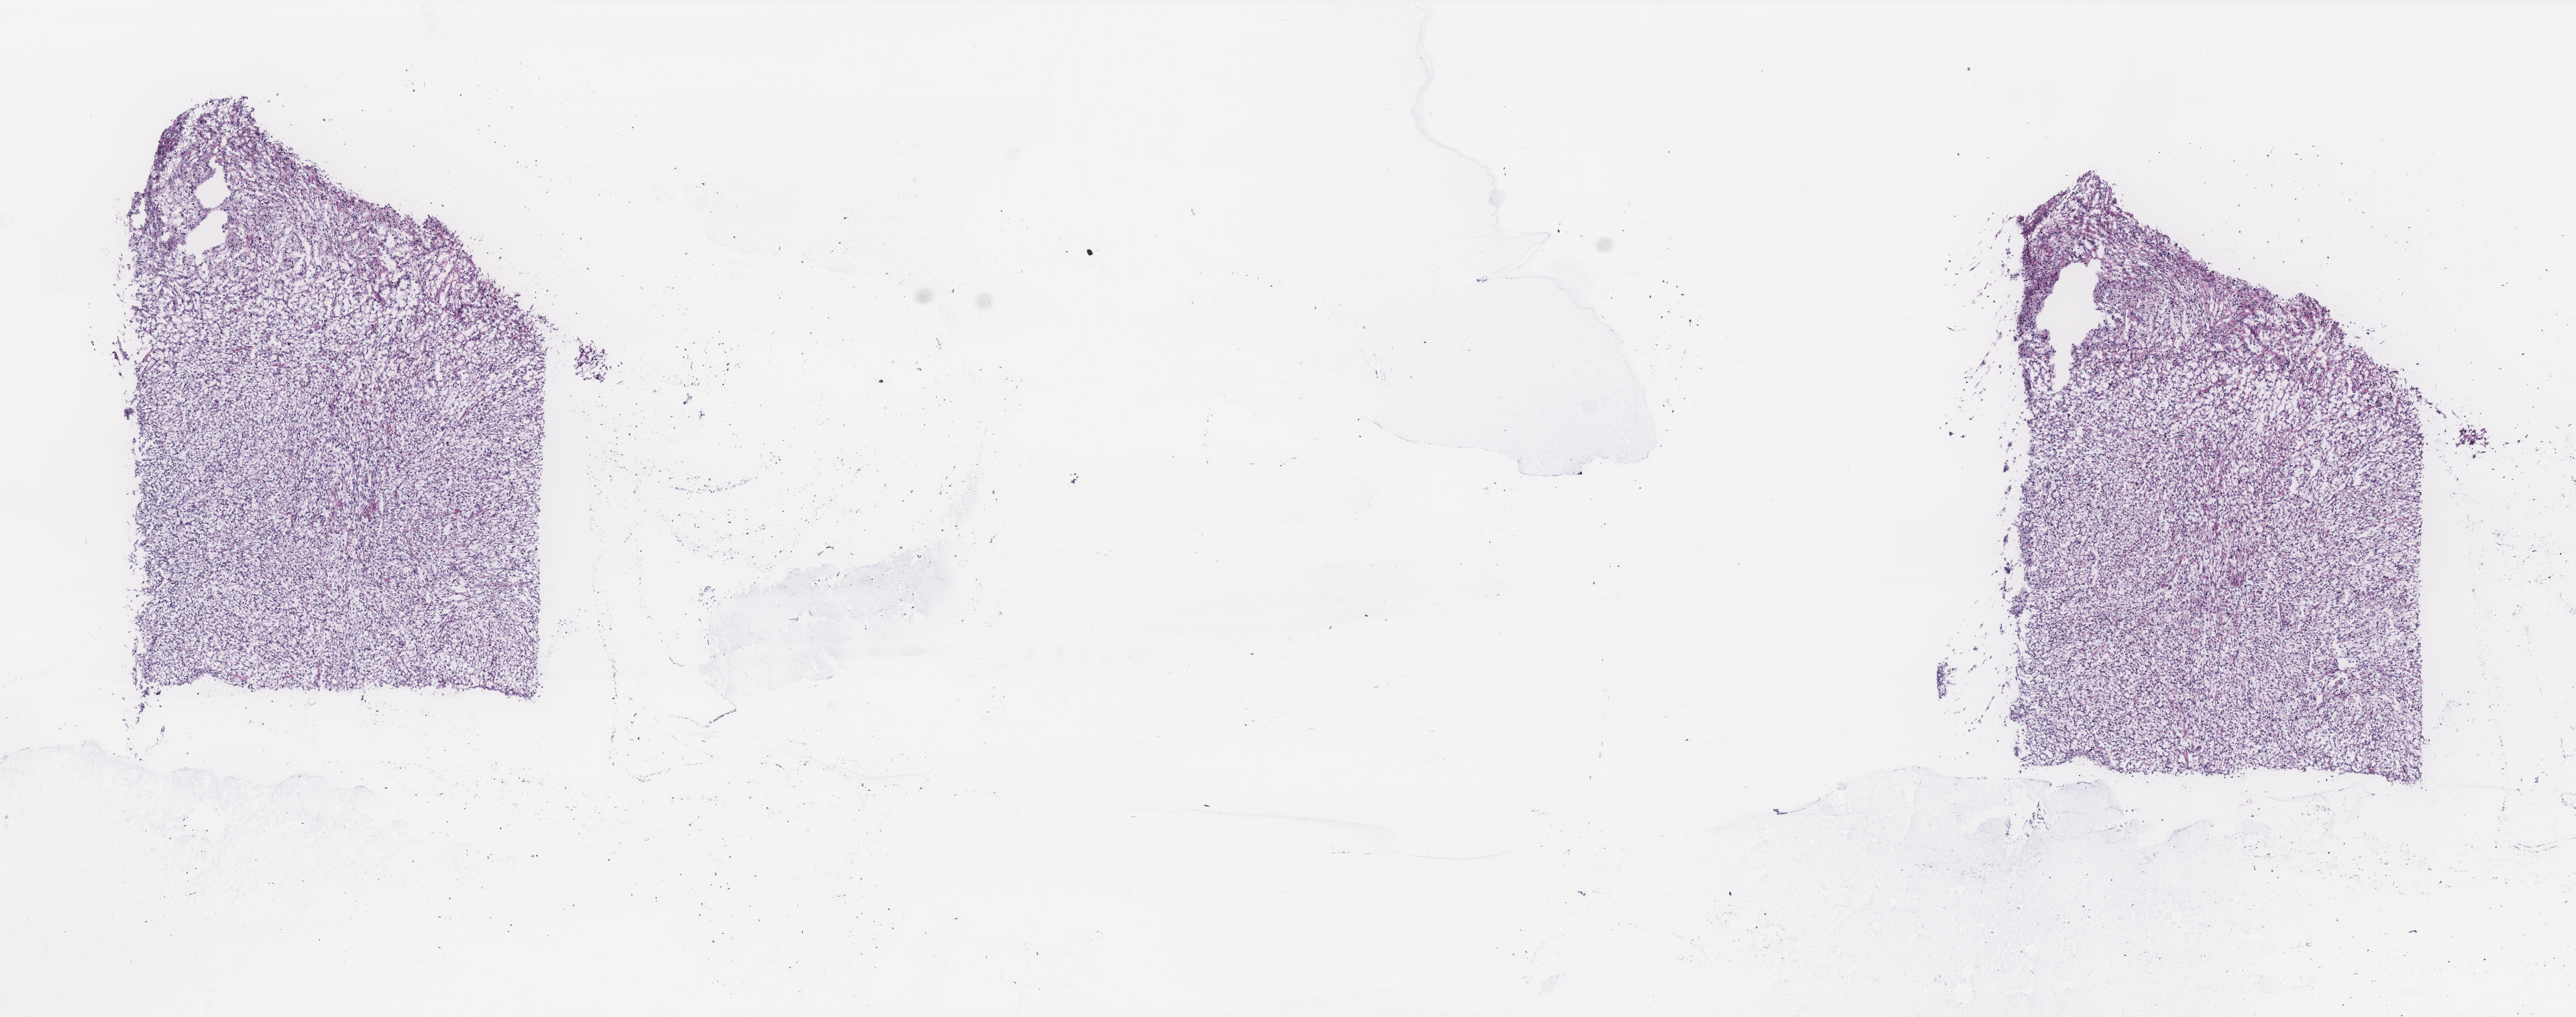
Whole-slide histology image, Hematoxylin and eosin (H&E) stained — shown as a low-resolution overview of the whole scanned area (about 15.4 x 6.1 mm). Frozen section from the top of the tissue portion. Primary tumour sample from the retroperitoneum and peritoneum. Male patient; age at initial diagnosis 66 years. Composition of this section per pathologist review: tumour cells 90%, tumour nuclei 90%, normal cells 0%, stromal cells 10%, necrosis 0%. Infiltration values recorded for this section: lymphocyte infiltration 2%, monocyte infiltration 1%, neutrophil infiltration 1%.
Diagnosis: Dedifferentiated liposarcoma.